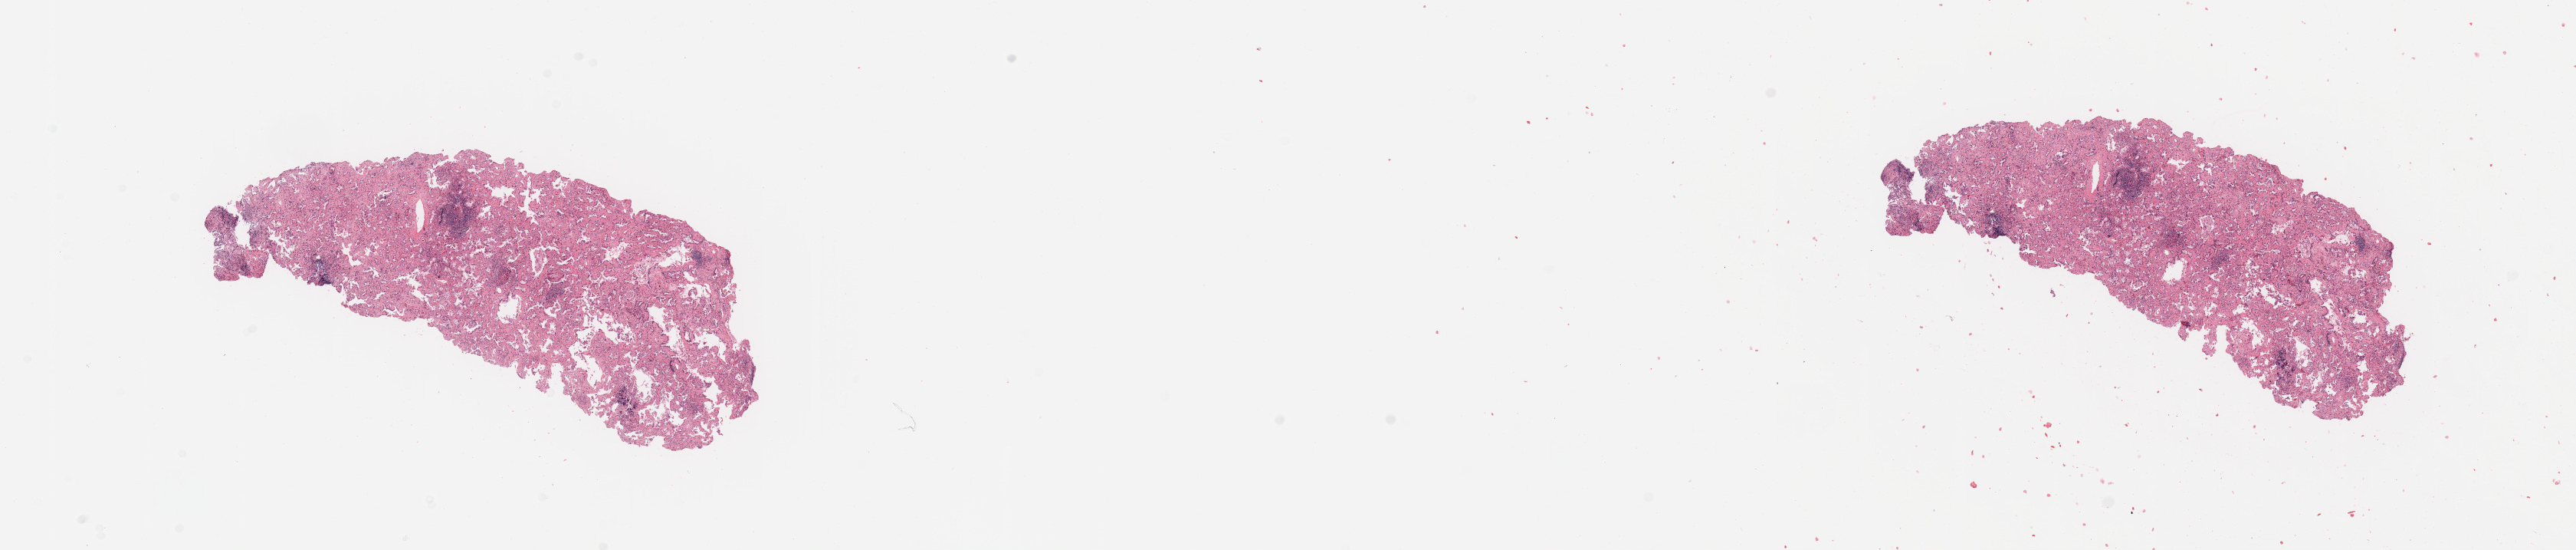
H&E-stained whole-slide image, a low-resolution overview of the entire scanned area, about 26.6 x 5.7 mm, lung, tissue type not recorded.
Patient diagnosis (cohort enrolment): lung adenocarcinoma (lung).